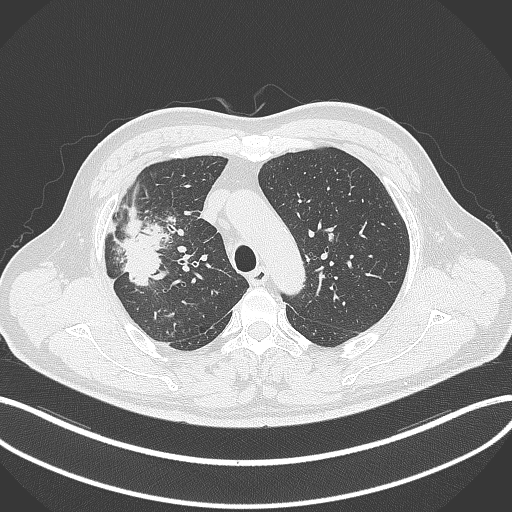
Chest CT, one axial slice. Reconstruction kernel B70f. 120 kVp. Lung window (W 1500 / L -600 HU). 512 × 512 image matrix, field of view 400 × 400 mm. Patient: male, 55 years. From the clinical record (not read from this slice): clinical TNM (as recorded): T3 N2 M1.
Outlined on this slice (bounding box drawn by a radiologist):
- lung tumour (recorded histology: adenocarcinoma): bounding box [x1, y1, x2, y2] px = [115, 213, 170, 287]